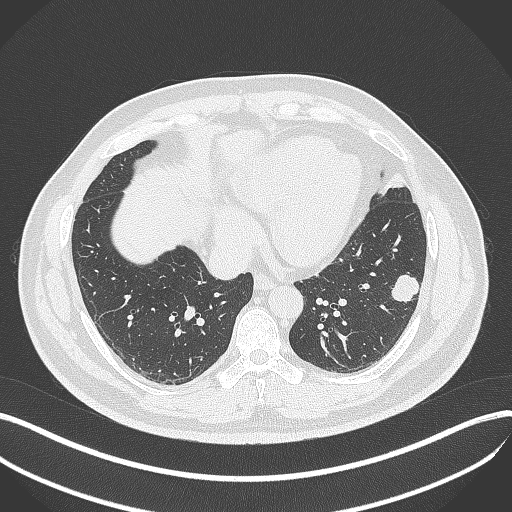
Chest CT, one axial slice. Slice 145 of 429 in the series (ordered by position). Reconstruction kernel B70f. 120 kVp. Lung window (W 1500 / L -600 HU). 512 × 512 image matrix. Male patient, age 39 years. From the clinical record (not read from this slice): clinical TNM (as recorded): T2a N0 M0.
Outlined on this slice (rectangle marked by the reading radiologist):
- lung tumour (recorded histology: adenocarcinoma): box from (x=386, y=269) to (x=423, y=307) px